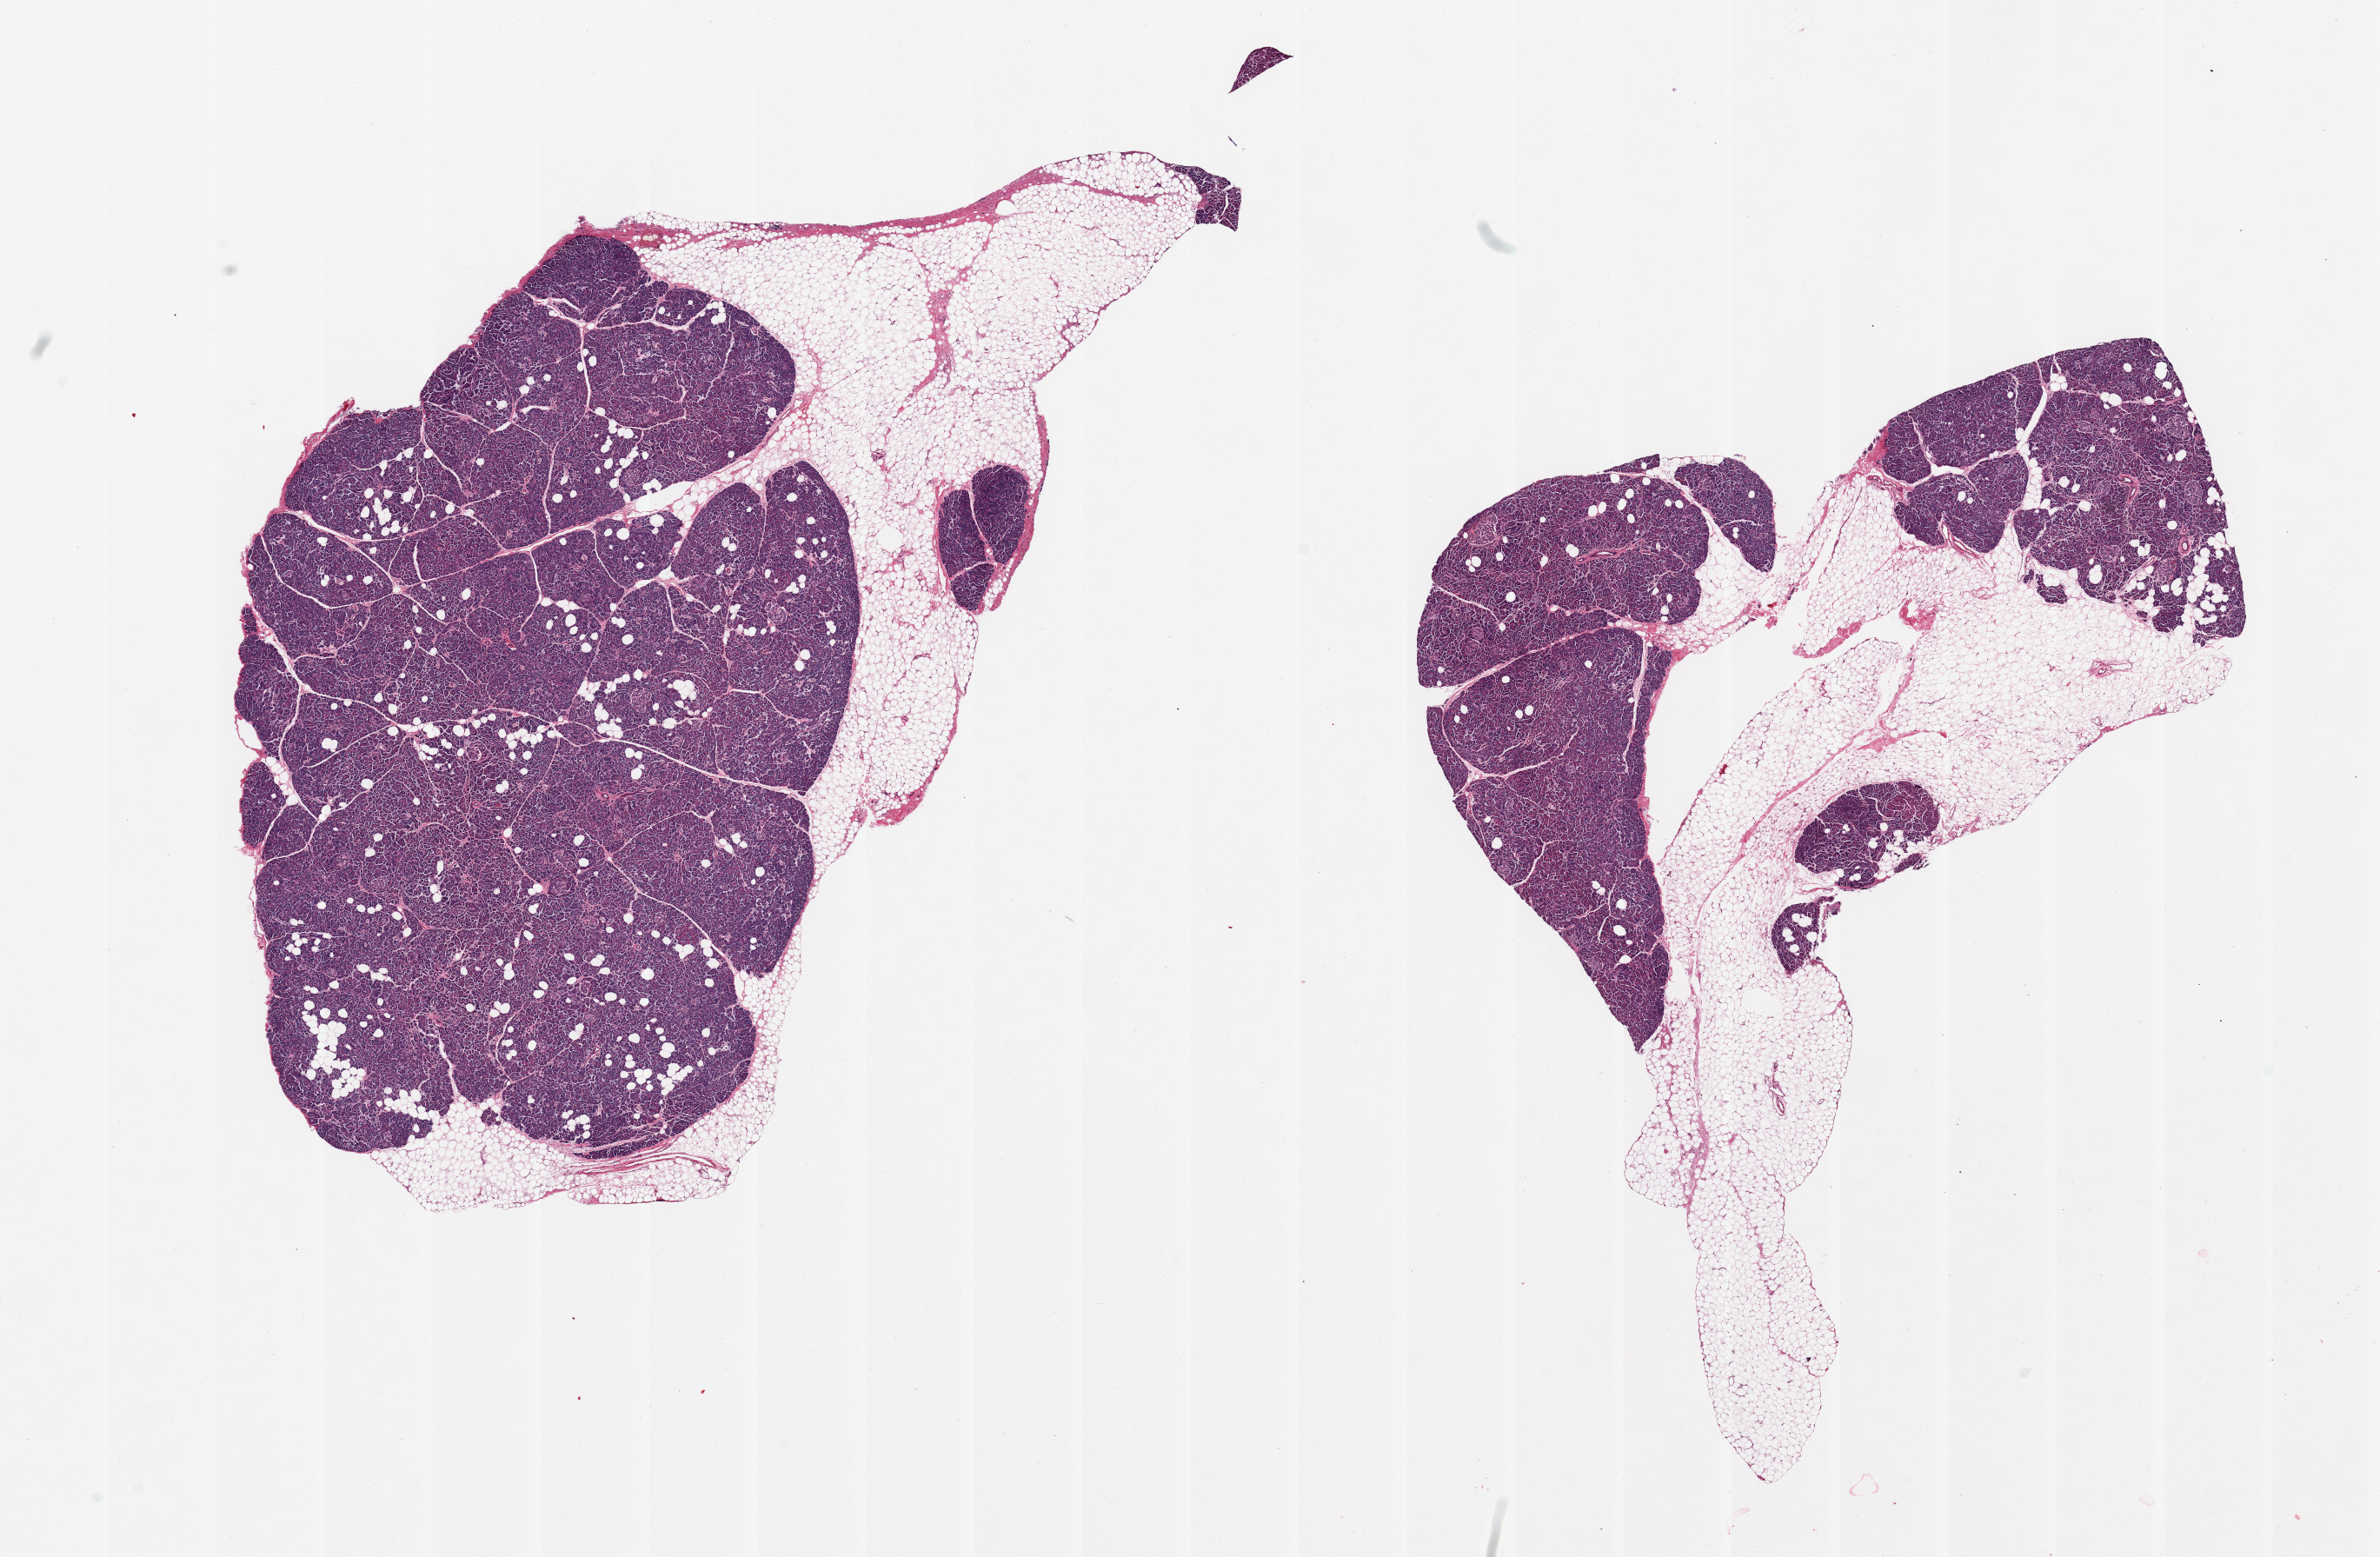
Hematoxylin and eosin (H&E) whole-slide image — a low-resolution overview of the entire scanned area, about 21.7 x 14.2 mm (acquisition: 20x scan), PAXgene-fixed paraffin-embedded (PFPE) section, target tissue: pancreas, tissue donor sample. Donor sex: male.
Review note (as recorded): 2 pieces; 30 & 50% adipose content.